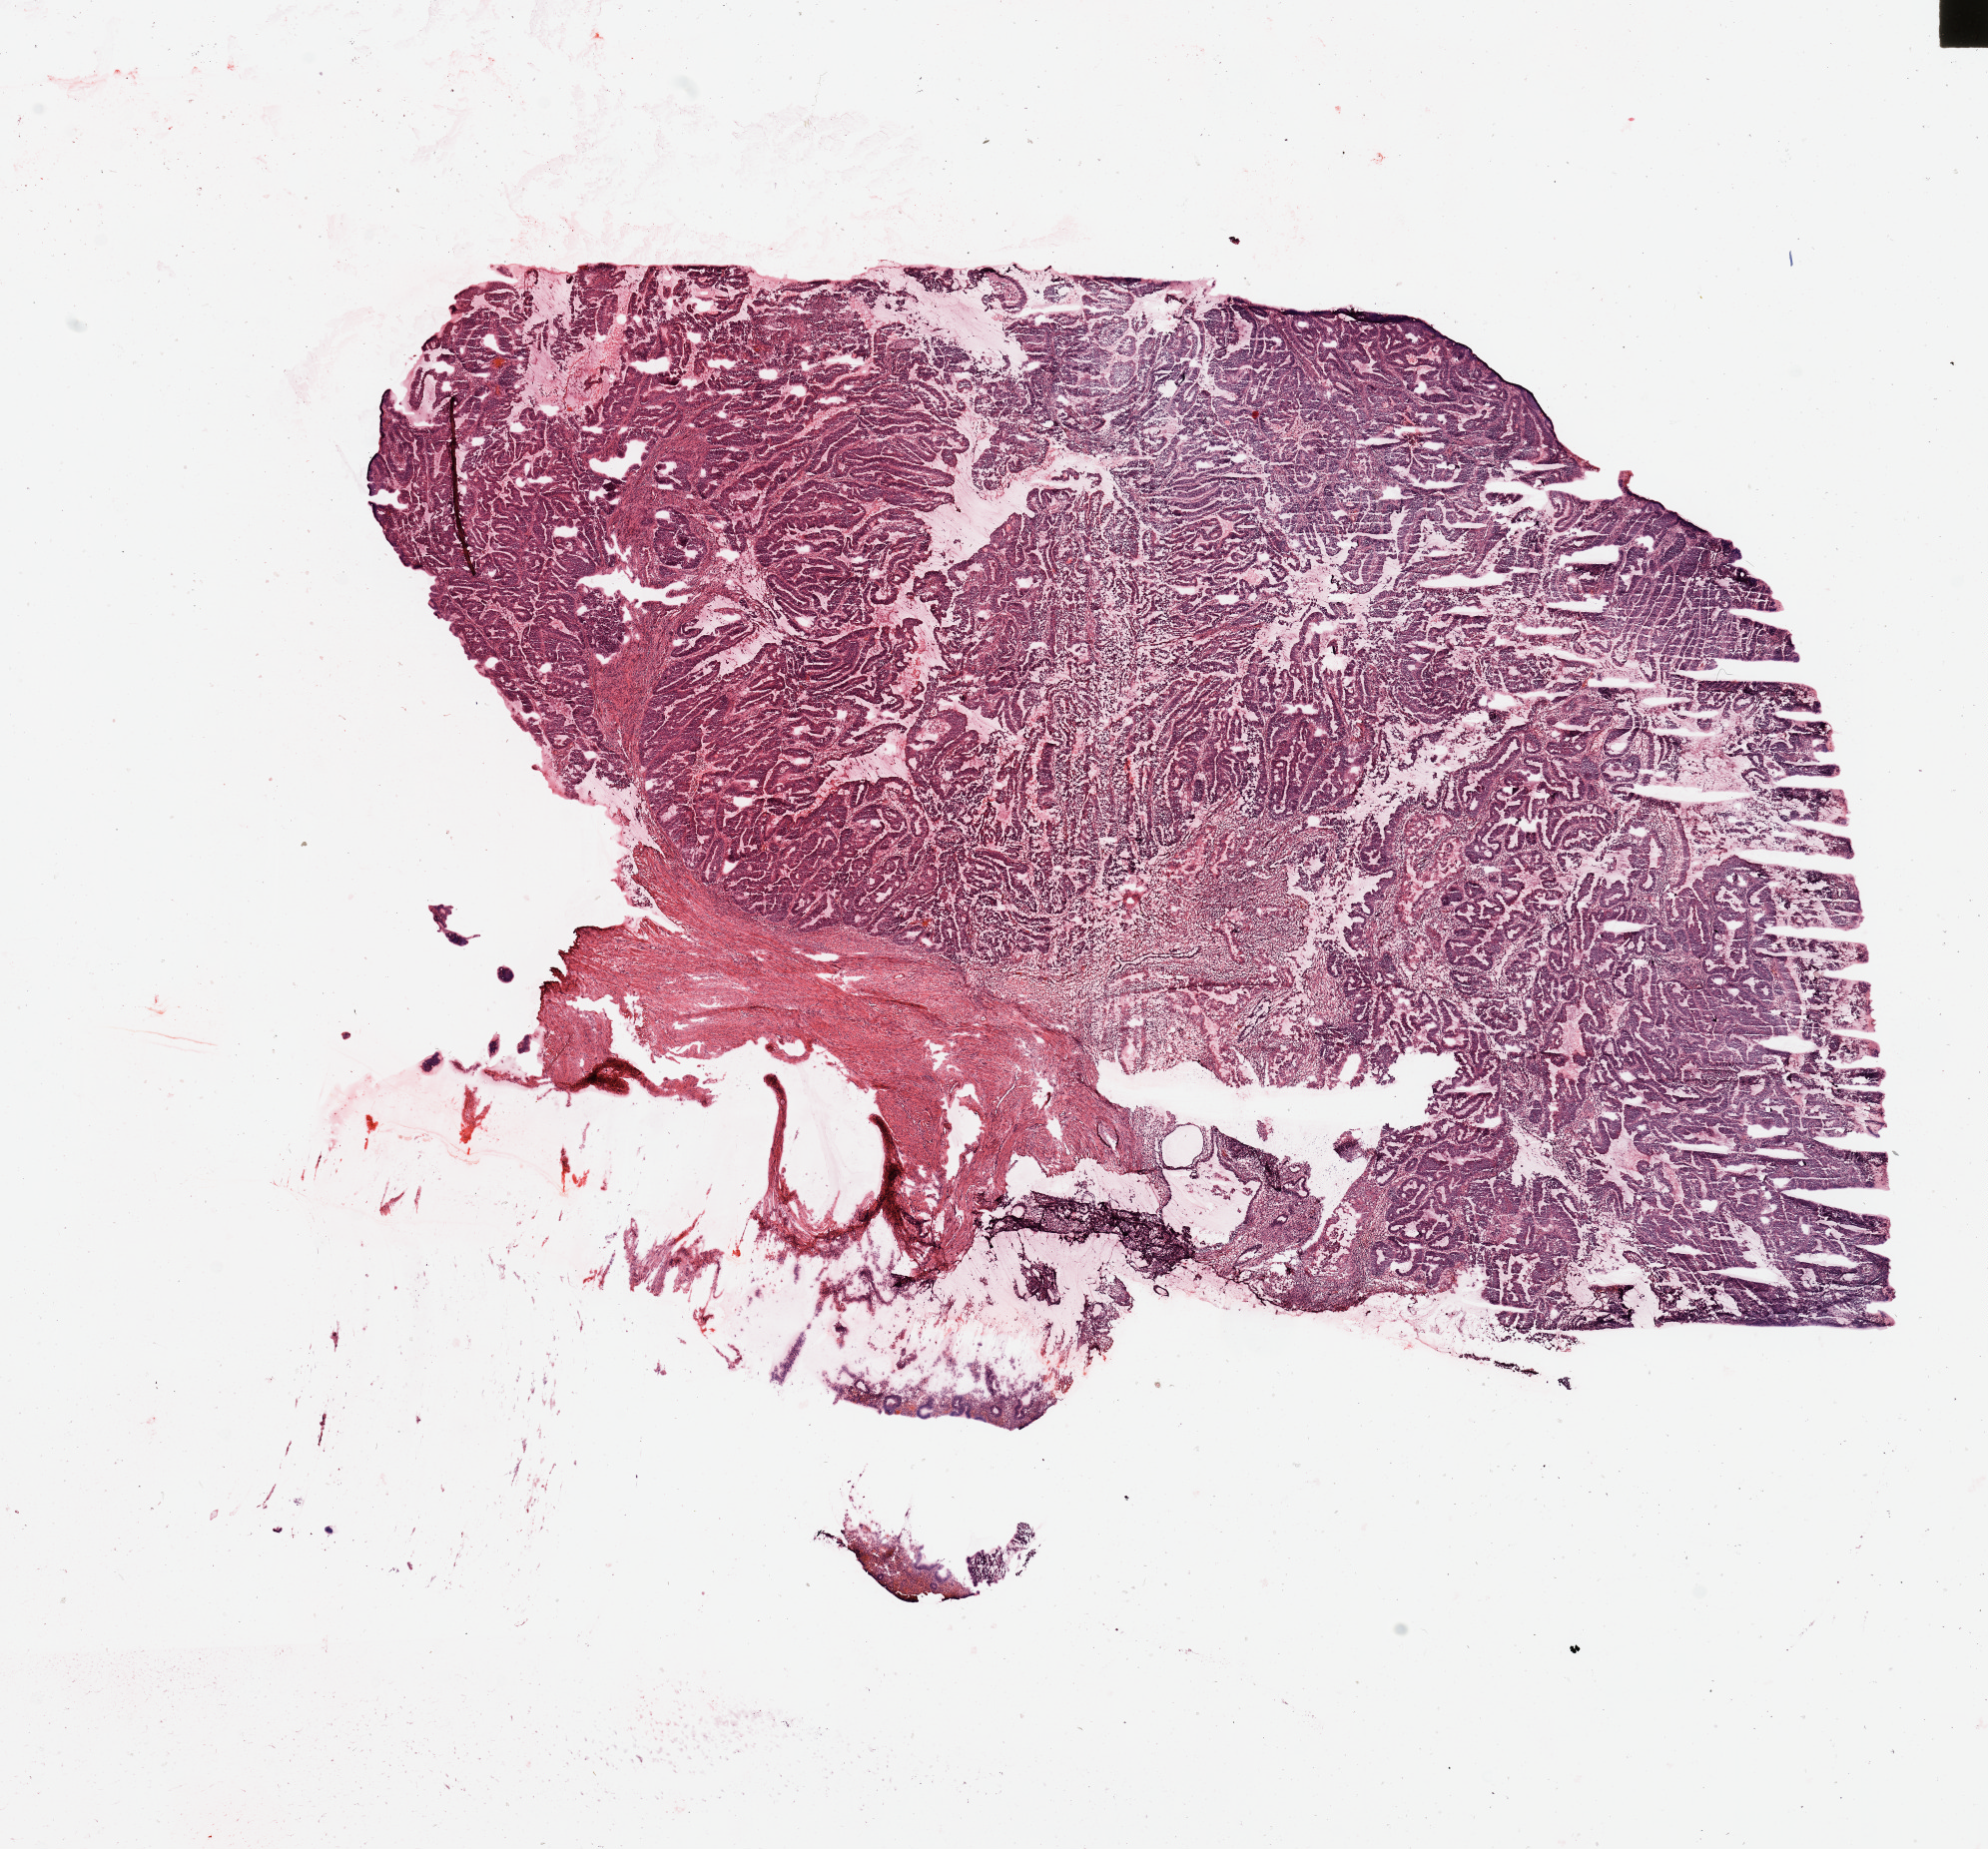
H&E whole-slide image — shown as a low-resolution overview of the whole scanned area (about 15.8 x 14.7 mm, slide scanned at 20x). Tumour tissue sample, uterus. Patient: female, age 45 years. Histologic grade: G1 (well differentiated).
- AJCC pathologic stage: I
- diagnosis: Endometrioid adenocarcinoma, NOS